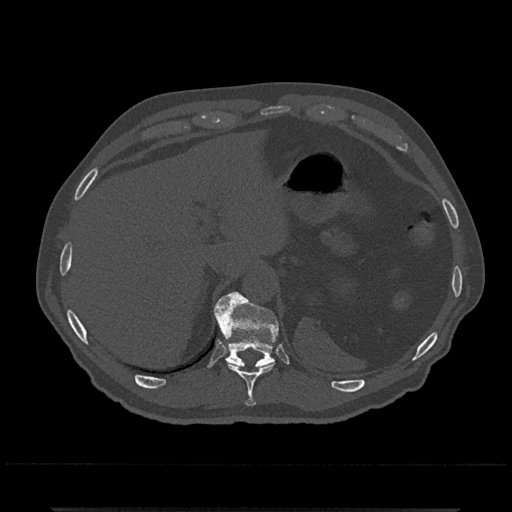
CT including the spine, one axial slice; slice 525 of 797 in the series (ordered by position); reconstruction kernel Br40s/3; bone window (W 1800 / L 400 HU); 0.5 mm slice thickness; 512 × 512 image matrix, field of view 393 × 393 mm. Male patient, age 67 years. Case-level facts recorded for this patient, not image findings: primary cancer: prostate.
Structures marked on this image (semi-automatic segmentation, software-assisted and operator-edited):
- T10 vertebra: bounding box <230,364,274,407> (left, top, right, bottom; pixels)
- T11 vertebra: <214,292,279,368>